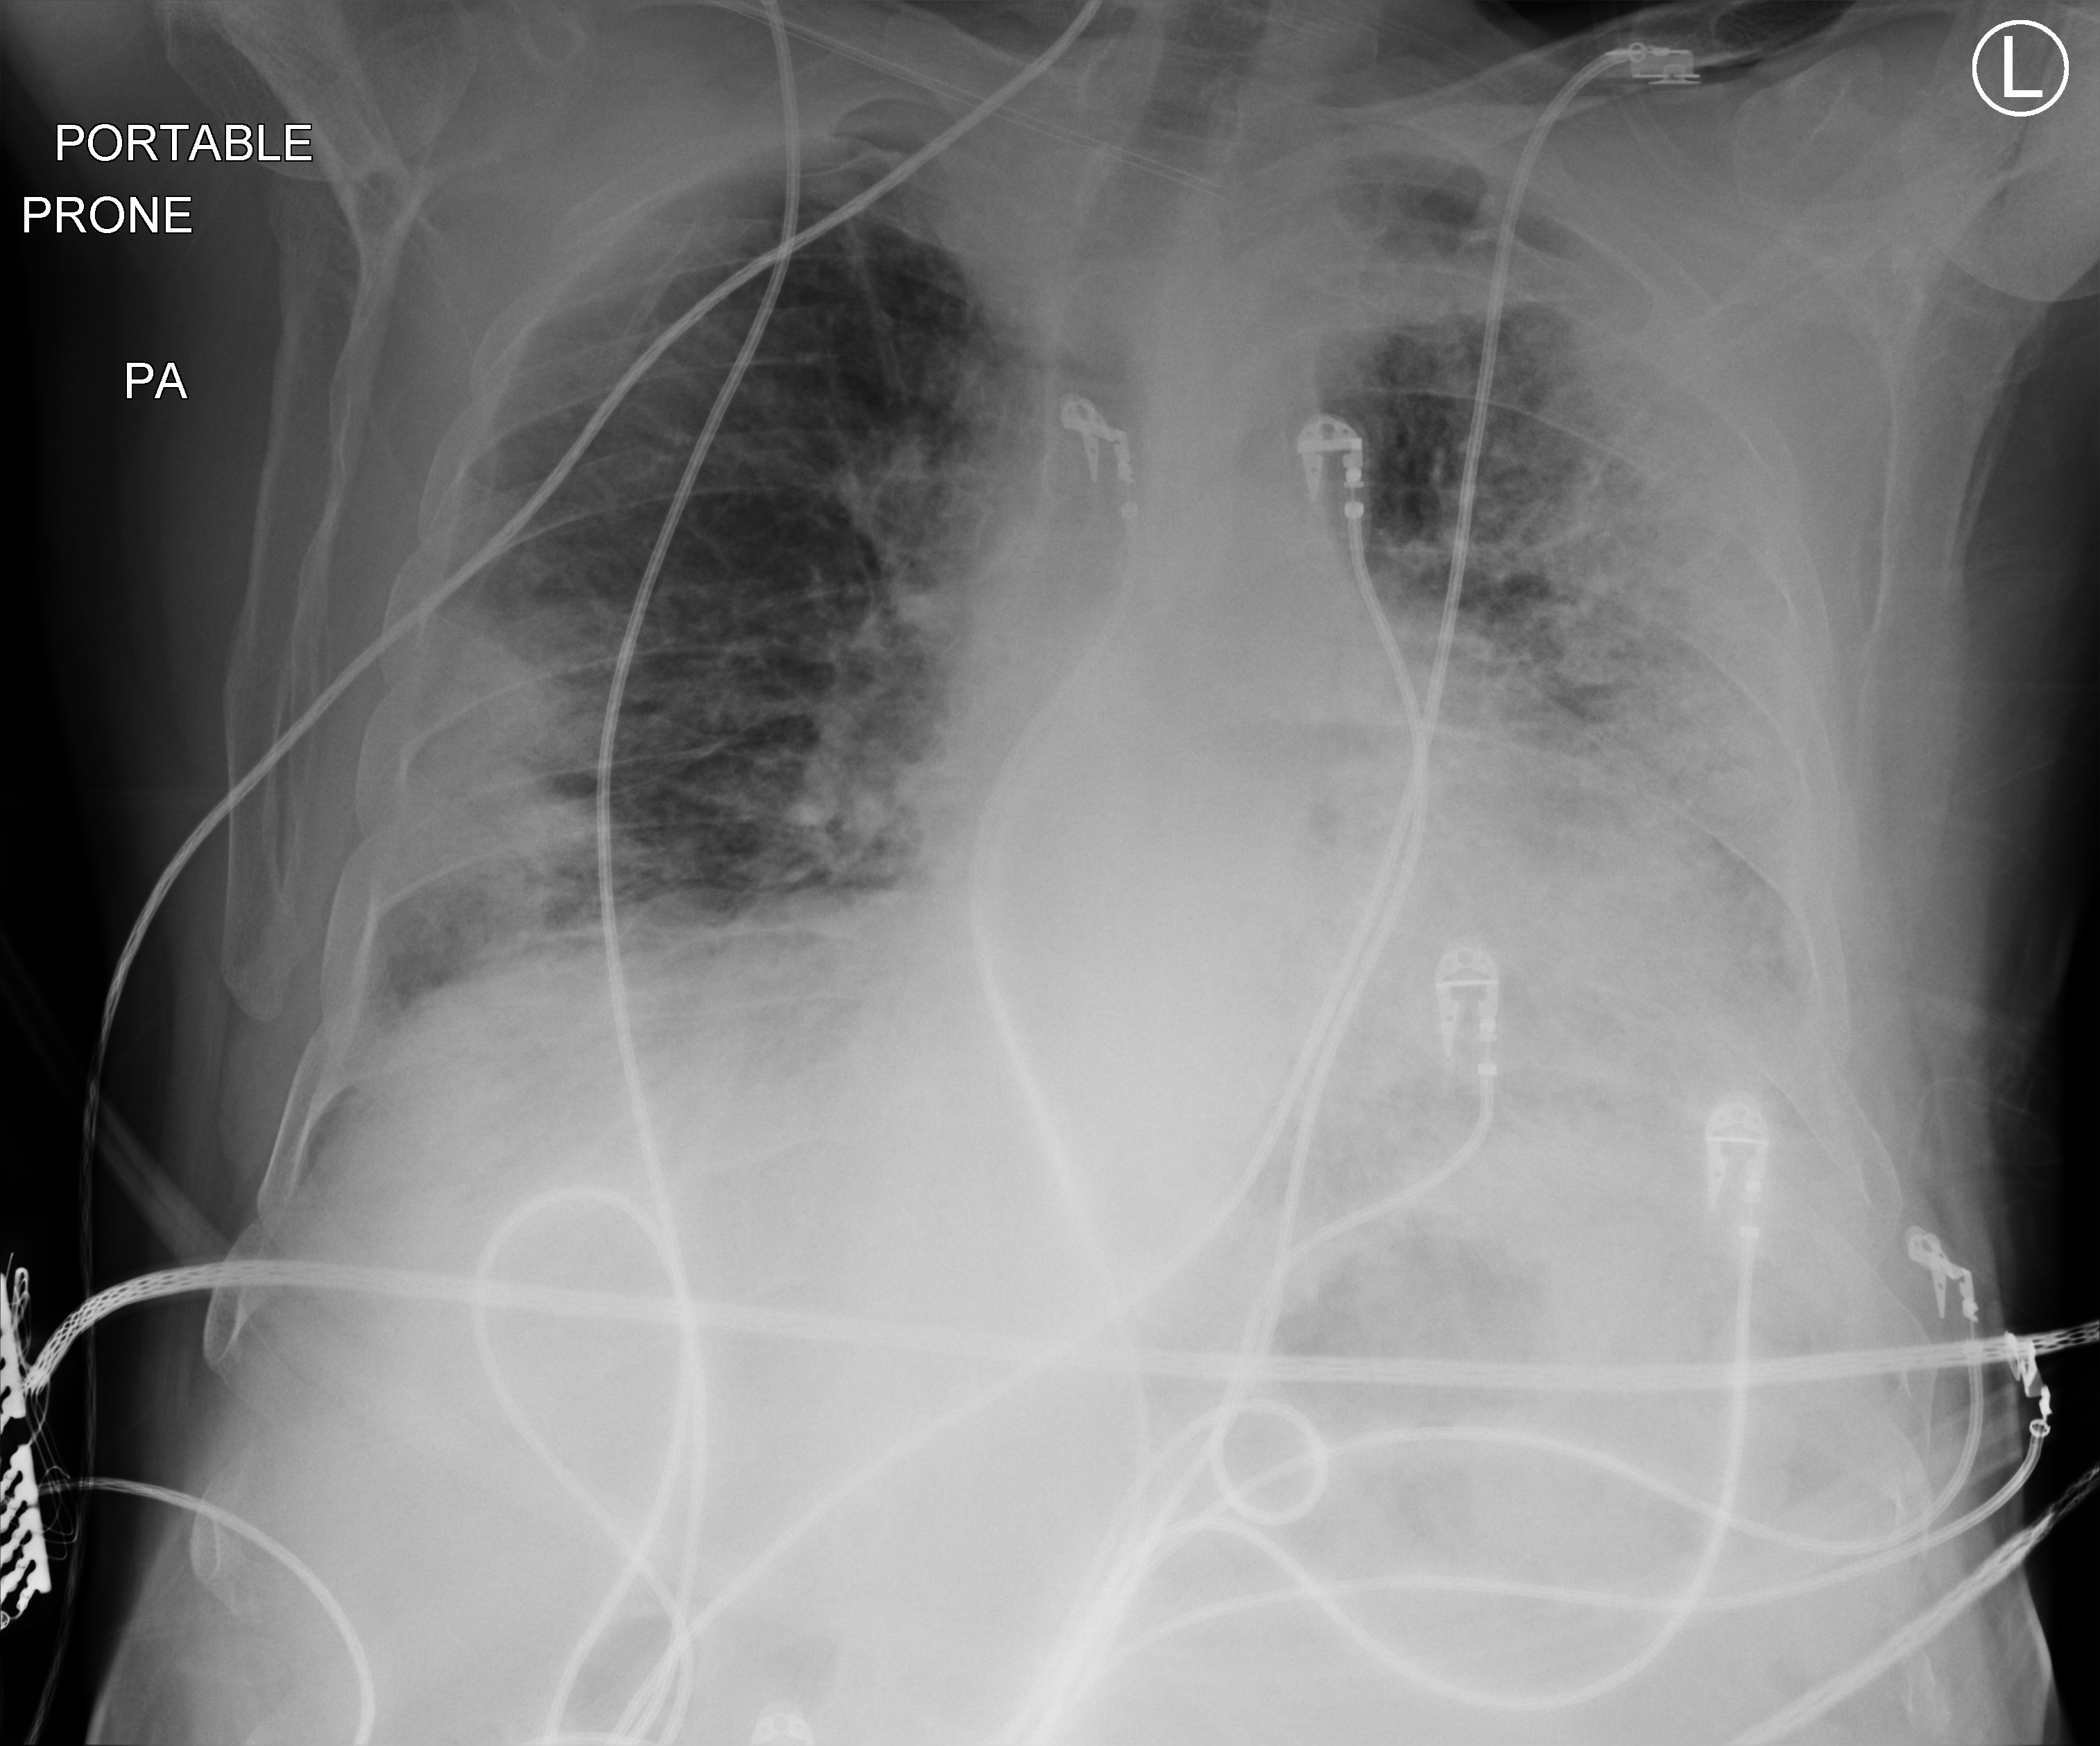
Bedside chest radiograph (computed radiography), posteroanterior (PA) projection. Patient hospitalised with COVID-19; male, aged 60–74 years.
Hospital-stay facts (about this admission, not read from this image; timing relative to this image not recorded): other chronic lung disease (admission record): no.